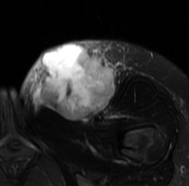
MRI of an extremity soft-tissue mass, one axial slice; slice 37 of 77 in the series (ordered by position); T2-weighted fat-saturated; MR volume resampled by the dataset authors to the PET/CT grid (not the native acquisition matrix); 3.27 mm slice thickness; 189 × 186 image matrix, field of view 185 × 182 mm. Female patient. Case-level facts recorded for this patient, not image findings: histological type: leiomyosarcoma; grade: high; site of the primary tumour: groin.
Outlined on this slice (expert contour drawn on MRI and transferred to this co-registered scan by the dataset authors):
- gross tumour volume including surrounding oedema: box from (x=19, y=40) to (x=132, y=124) px
- gross tumour volume (mass): (x=33, y=43)–(x=114, y=121)